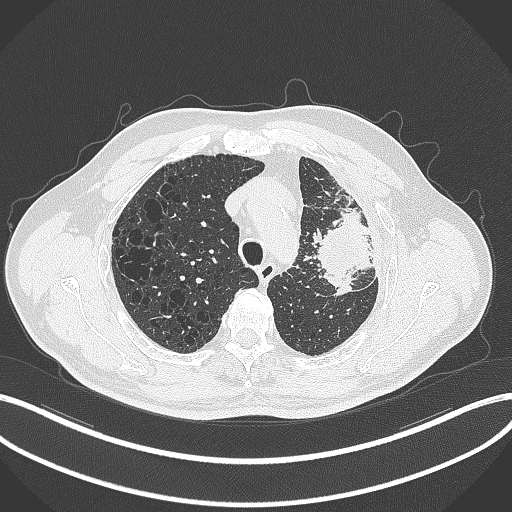
Chest CT, one axial slice; slice 248 of 297 in the series (ordered by position); reconstruction kernel B70f; lung window (W 1500 / L -600 HU); 1 mm slice thickness; 512 × 512 image matrix, field of view 400 × 400 mm. Male patient, age 68 years. From the clinical record (not read from this slice): clinical TNM (as recorded): T3 N3 M1.
Outlined on this slice (bounding box drawn by a radiologist):
- lung tumour (recorded histology: adenocarcinoma): bounding box (x1, y1, x2, y2) in pixels: (311, 196, 372, 300)